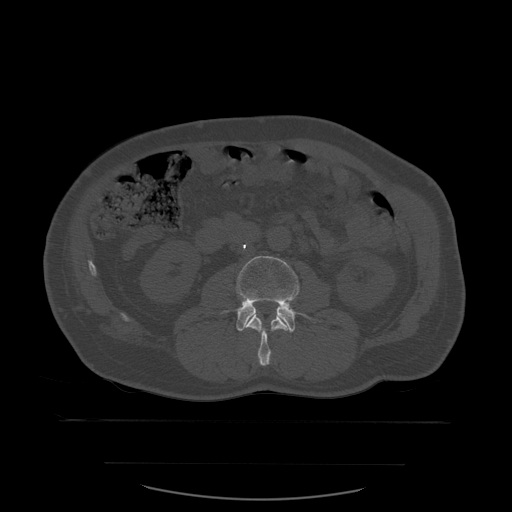
CT including the spine, one axial slice. Bone window (W 1800 / L 400 HU). 512 × 512 image matrix. Patient age 71 years. Case-level facts recorded for this patient, not image findings: primary cancer: lung; vertebrae with lytic lesions (as recorded): T1, T2, L5, S1.
Annotated regions visible in this slice (semi-automatic segmentation, software-assisted and operator-edited):
- L2 vertebra: box from (x=245, y=310) to (x=290, y=366) px
- L3 vertebra: (x=221, y=256)–(x=318, y=333)